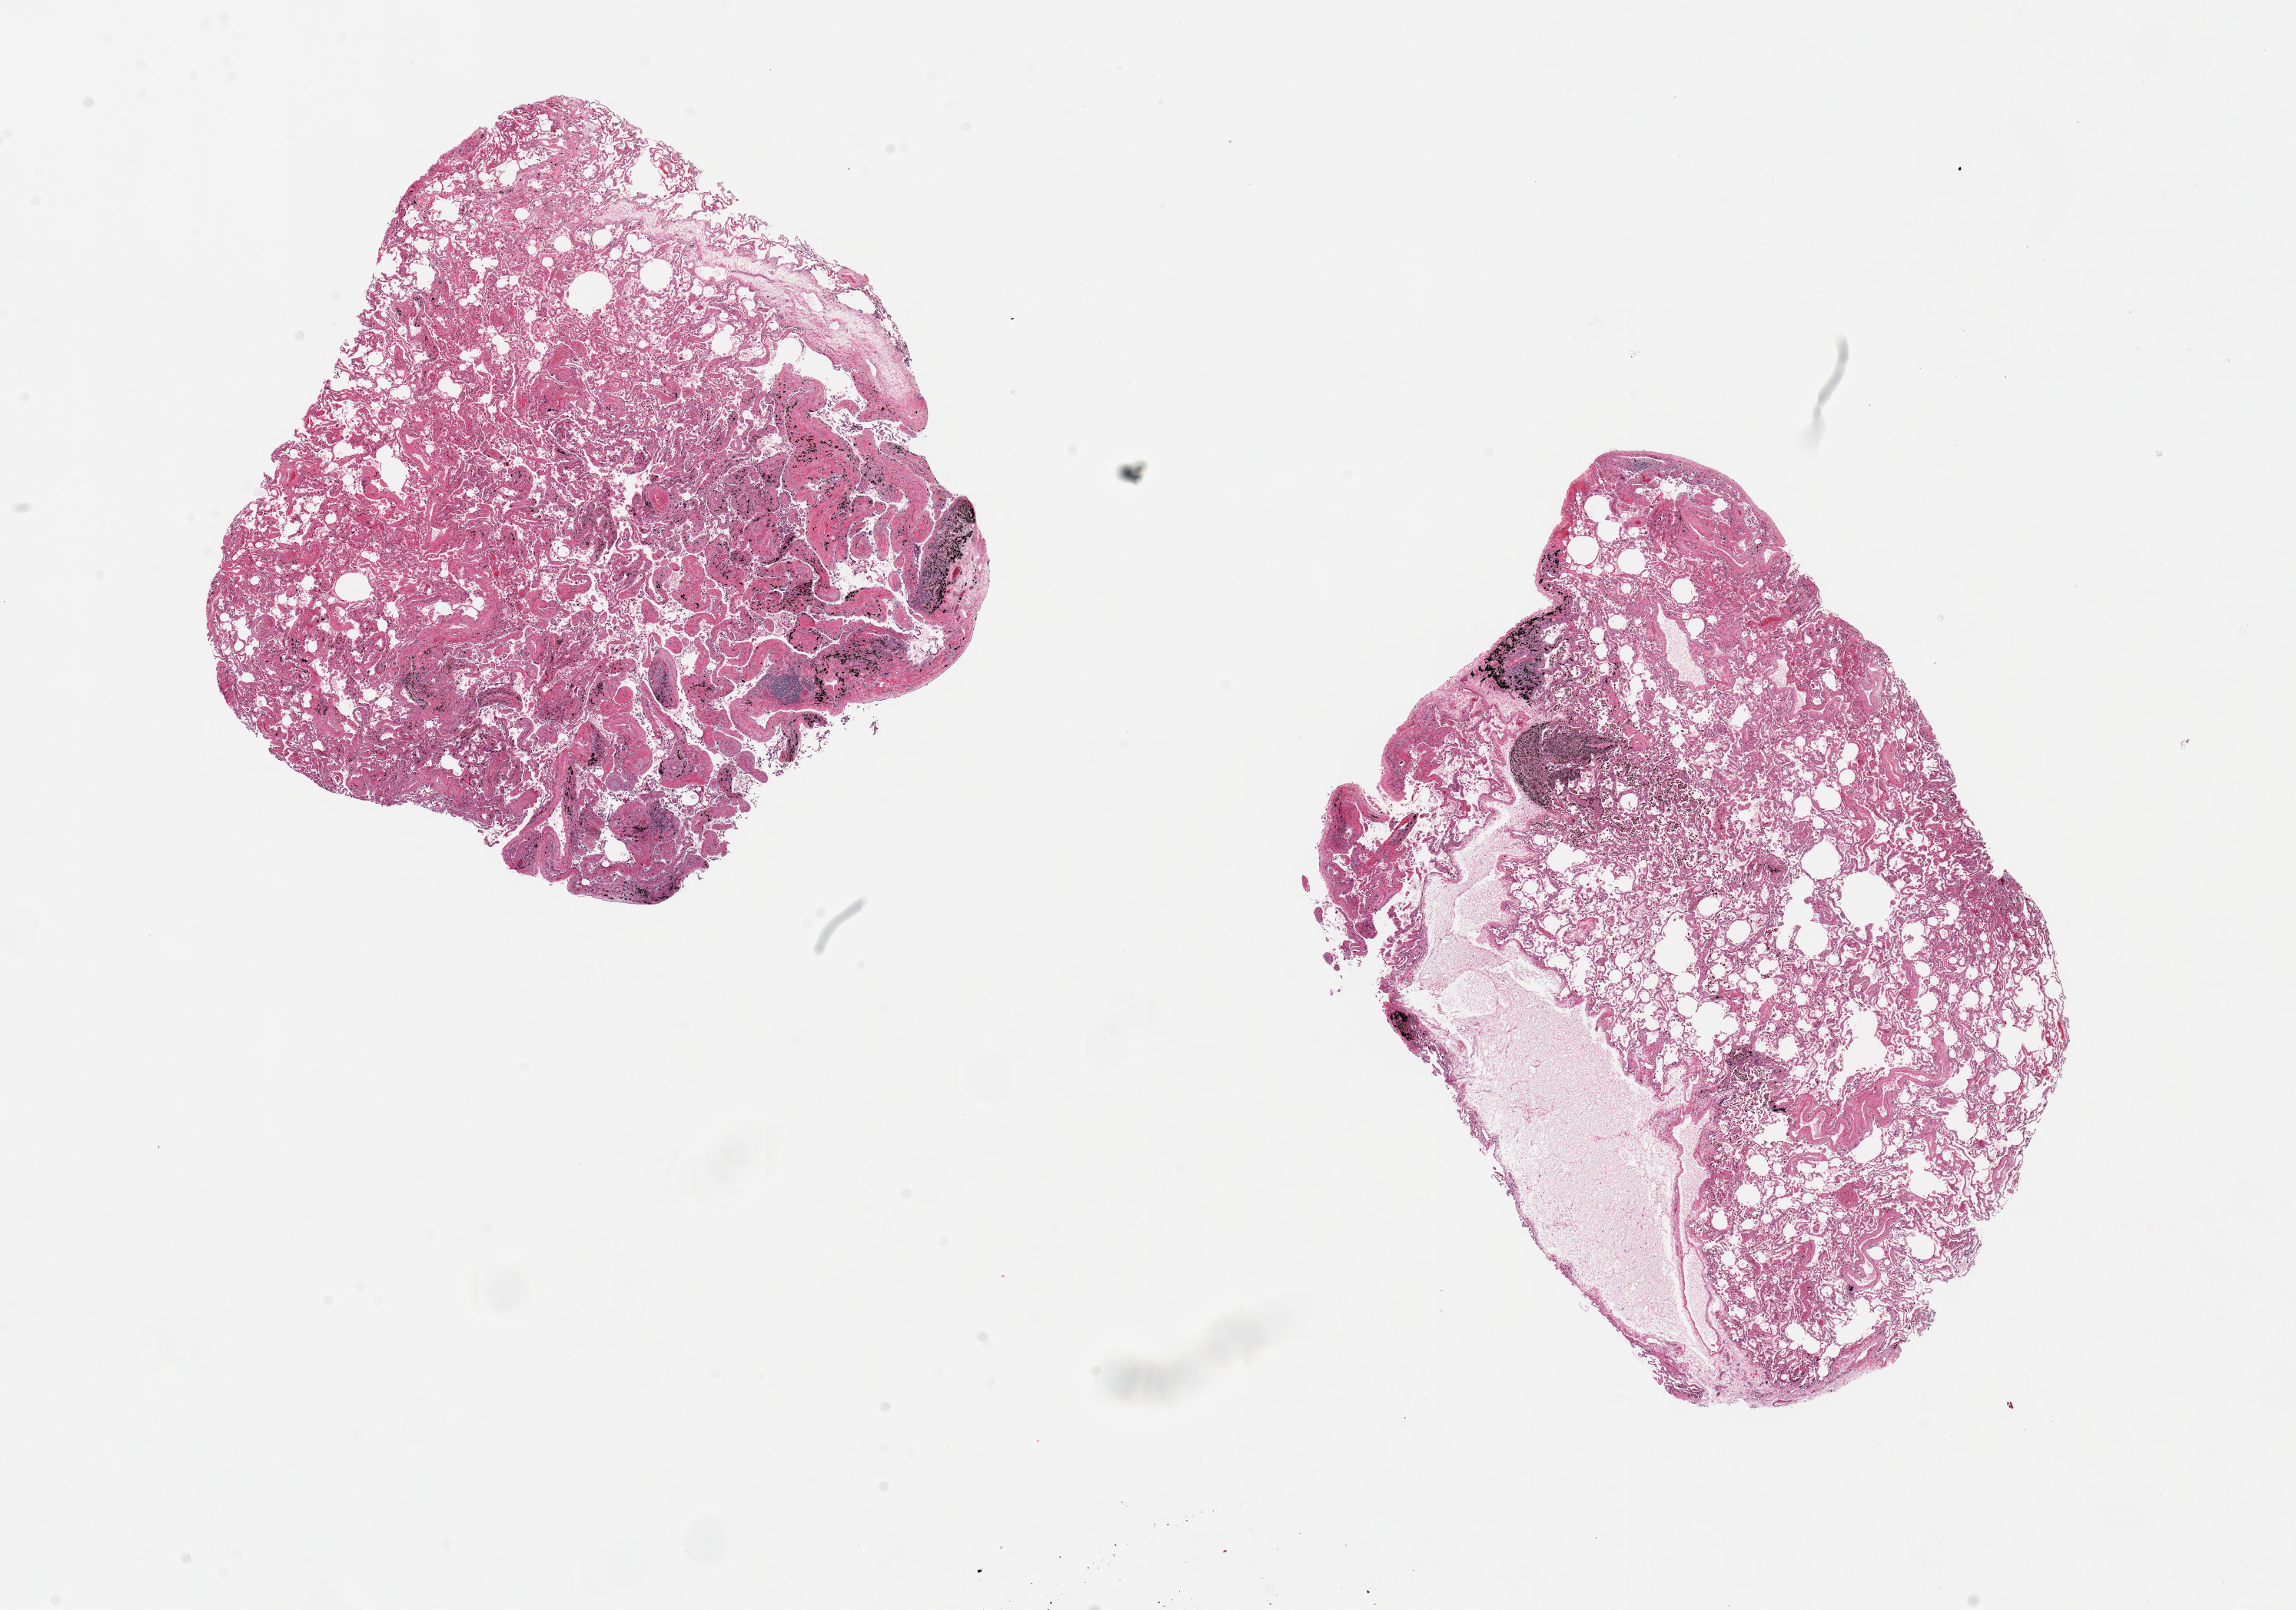
Whole-slide image, hematoxylin and eosin (H&E) stain, brightfield — low-resolution overview of the scanned area, about 23.6 x 16.6 mm. PAXgene-fixed paraffin-embedded (PFPE) section. Sampled site (target tissue): lung. Donor tissue sample. Donor sex: male.
- reviewer comment on this tissue sample: 2 pieces. 7.5x7 & 10x7mm; patchy fibrinous alveolar deposits, aggregated of pigmented histiocytes present, either smoking or industrial exposure related